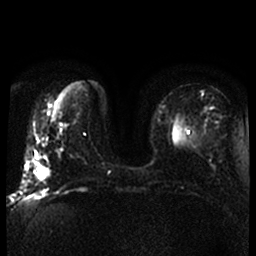
Breast MRI, one axial slice; slice 12 of 52 in the series (ordered by position); diffusion-weighted series; image 2 of 4 stored at this slice position (different b-values; order by instance number); 1.5 T; 4 mm slice thickness; 256 × 256 image matrix, field of view 320 × 320 mm. Female patient.
Structures marked on this image (outlined manually by an expert reader):
- tumour on diffusion-weighted imaging: bounding box <38,167,49,178> (left, top, right, bottom; pixels)